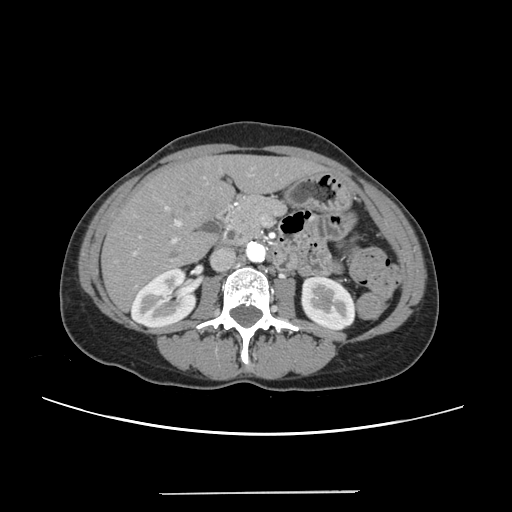
Contrast-enhanced abdominal CT, one axial slice; position 106 of 240 along the scan axis; 120 kVp; soft-tissue window (W 400 / L 40 HU); 1.25 mm slice thickness; 512 × 512 image matrix, field of view 371 × 371 mm. Female patient, age 60 years. From the clinical record (not read from this slice): diagnosis: colorectal cancer liver metastases, imaged before liver resection; multiple liver metastases: no; largest metastasis: 1.5 cm; disease in both lobes: no.
Annotated regions visible in this slice (outlined manually by an expert reader):
- liver: box from (x=104, y=157) to (x=318, y=308) px
- planned liver remnant (the part of the liver to remain after resection): (x=104, y=158)–(x=319, y=308)
- portal vein (with intrahepatic branches): (x=133, y=174)–(x=252, y=255)